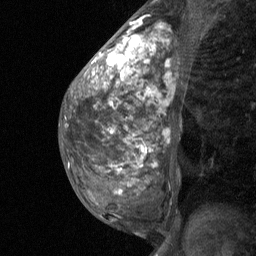
Breast MRI (dynamic contrast-enhanced), one sagittal slice. Slice 28 of 64 in the series (ordered by position). Dynamic contrast-enhanced study with each time point stored as its own series, time point 2 of 3 at this slice position (early post-contrast, ordered by acquisition time). 1.5 T. TE 4.8 ms, TR 27 ms. 256 × 256 image matrix. Female patient, age 36 years. From the clinical record (not read from this slice): setting: breast cancer imaged before/during neoadjuvant chemotherapy; receptor status: HR-positive, HER2-negative.
Outlined on this slice (semi-automatically segmented with operator editing):
- analysis volume of interest (the breast-tissue region the enhancement analysis was run in; not a lesion): box from (x=67, y=12) to (x=193, y=238) px
- tumour enhancement mask (voxels above the 90 % enhancement threshold inside the analysis volume of interest): (x=92, y=22)–(x=156, y=194)